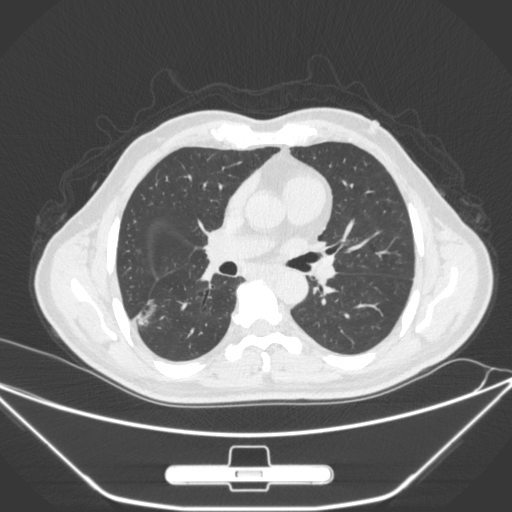
Chest CT, one axial slice. Position 157 of 310 along the scan axis. Lung window (W 1500 / L -600 HU). 1 mm slice thickness. 512 × 512 image matrix. Patient: male, 71 years. From the clinical record (not read from this slice): clinical TNM (as recorded): T1c N0 M0; histopathological grade: G2.
Structures marked on this image (rectangle marked by the reading radiologist):
- lung tumour (recorded histology: adenocarcinoma): bounding box (x1, y1, x2, y2) in pixels: (134, 295, 160, 329)